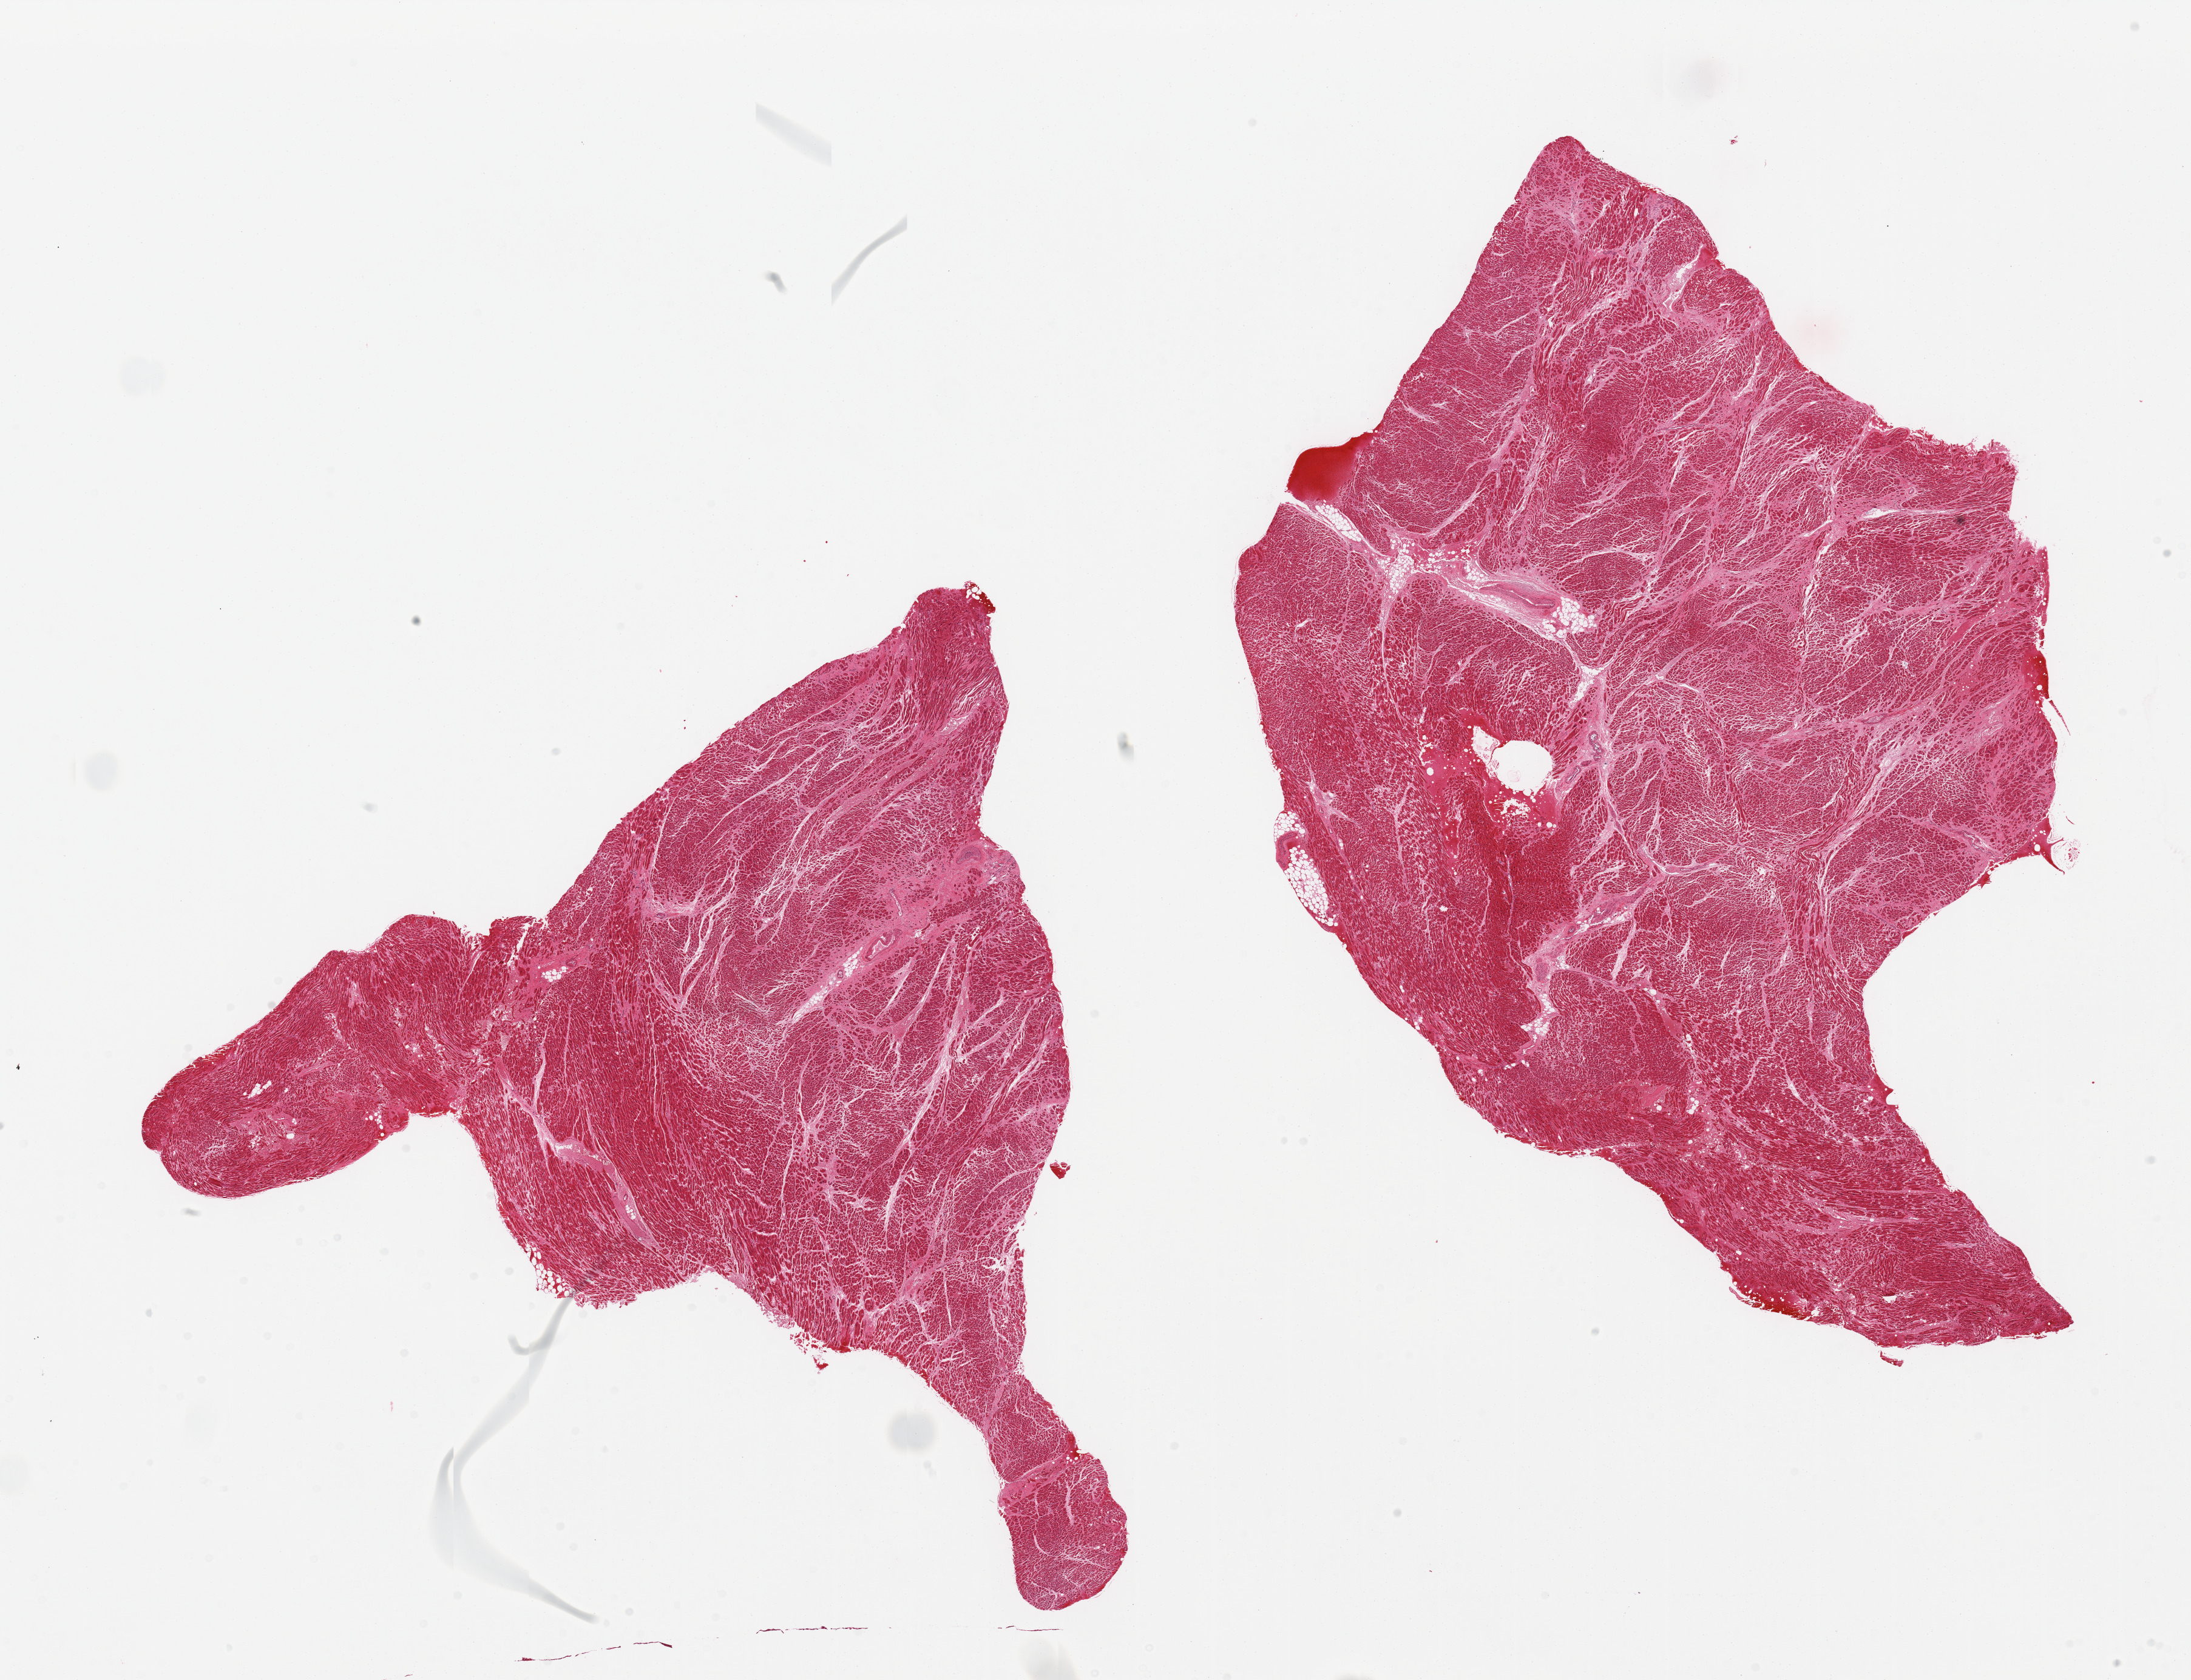
Whole-slide image, hematoxylin and eosin (H&E) stain, a low-resolution overview of the entire scanned area, about 28.5 x 21.9 mm (slide scanned at 20x); PAXgene-fixed paraffin-embedded (PFPE) section; section of heart (target tissue); tissue donor sample. Donor sex: male.
* pathologist's review note for this sample: 2 pieces, interstitial and patchy fibrosis, some boxcar nuclei (myocyte hypertrophy)